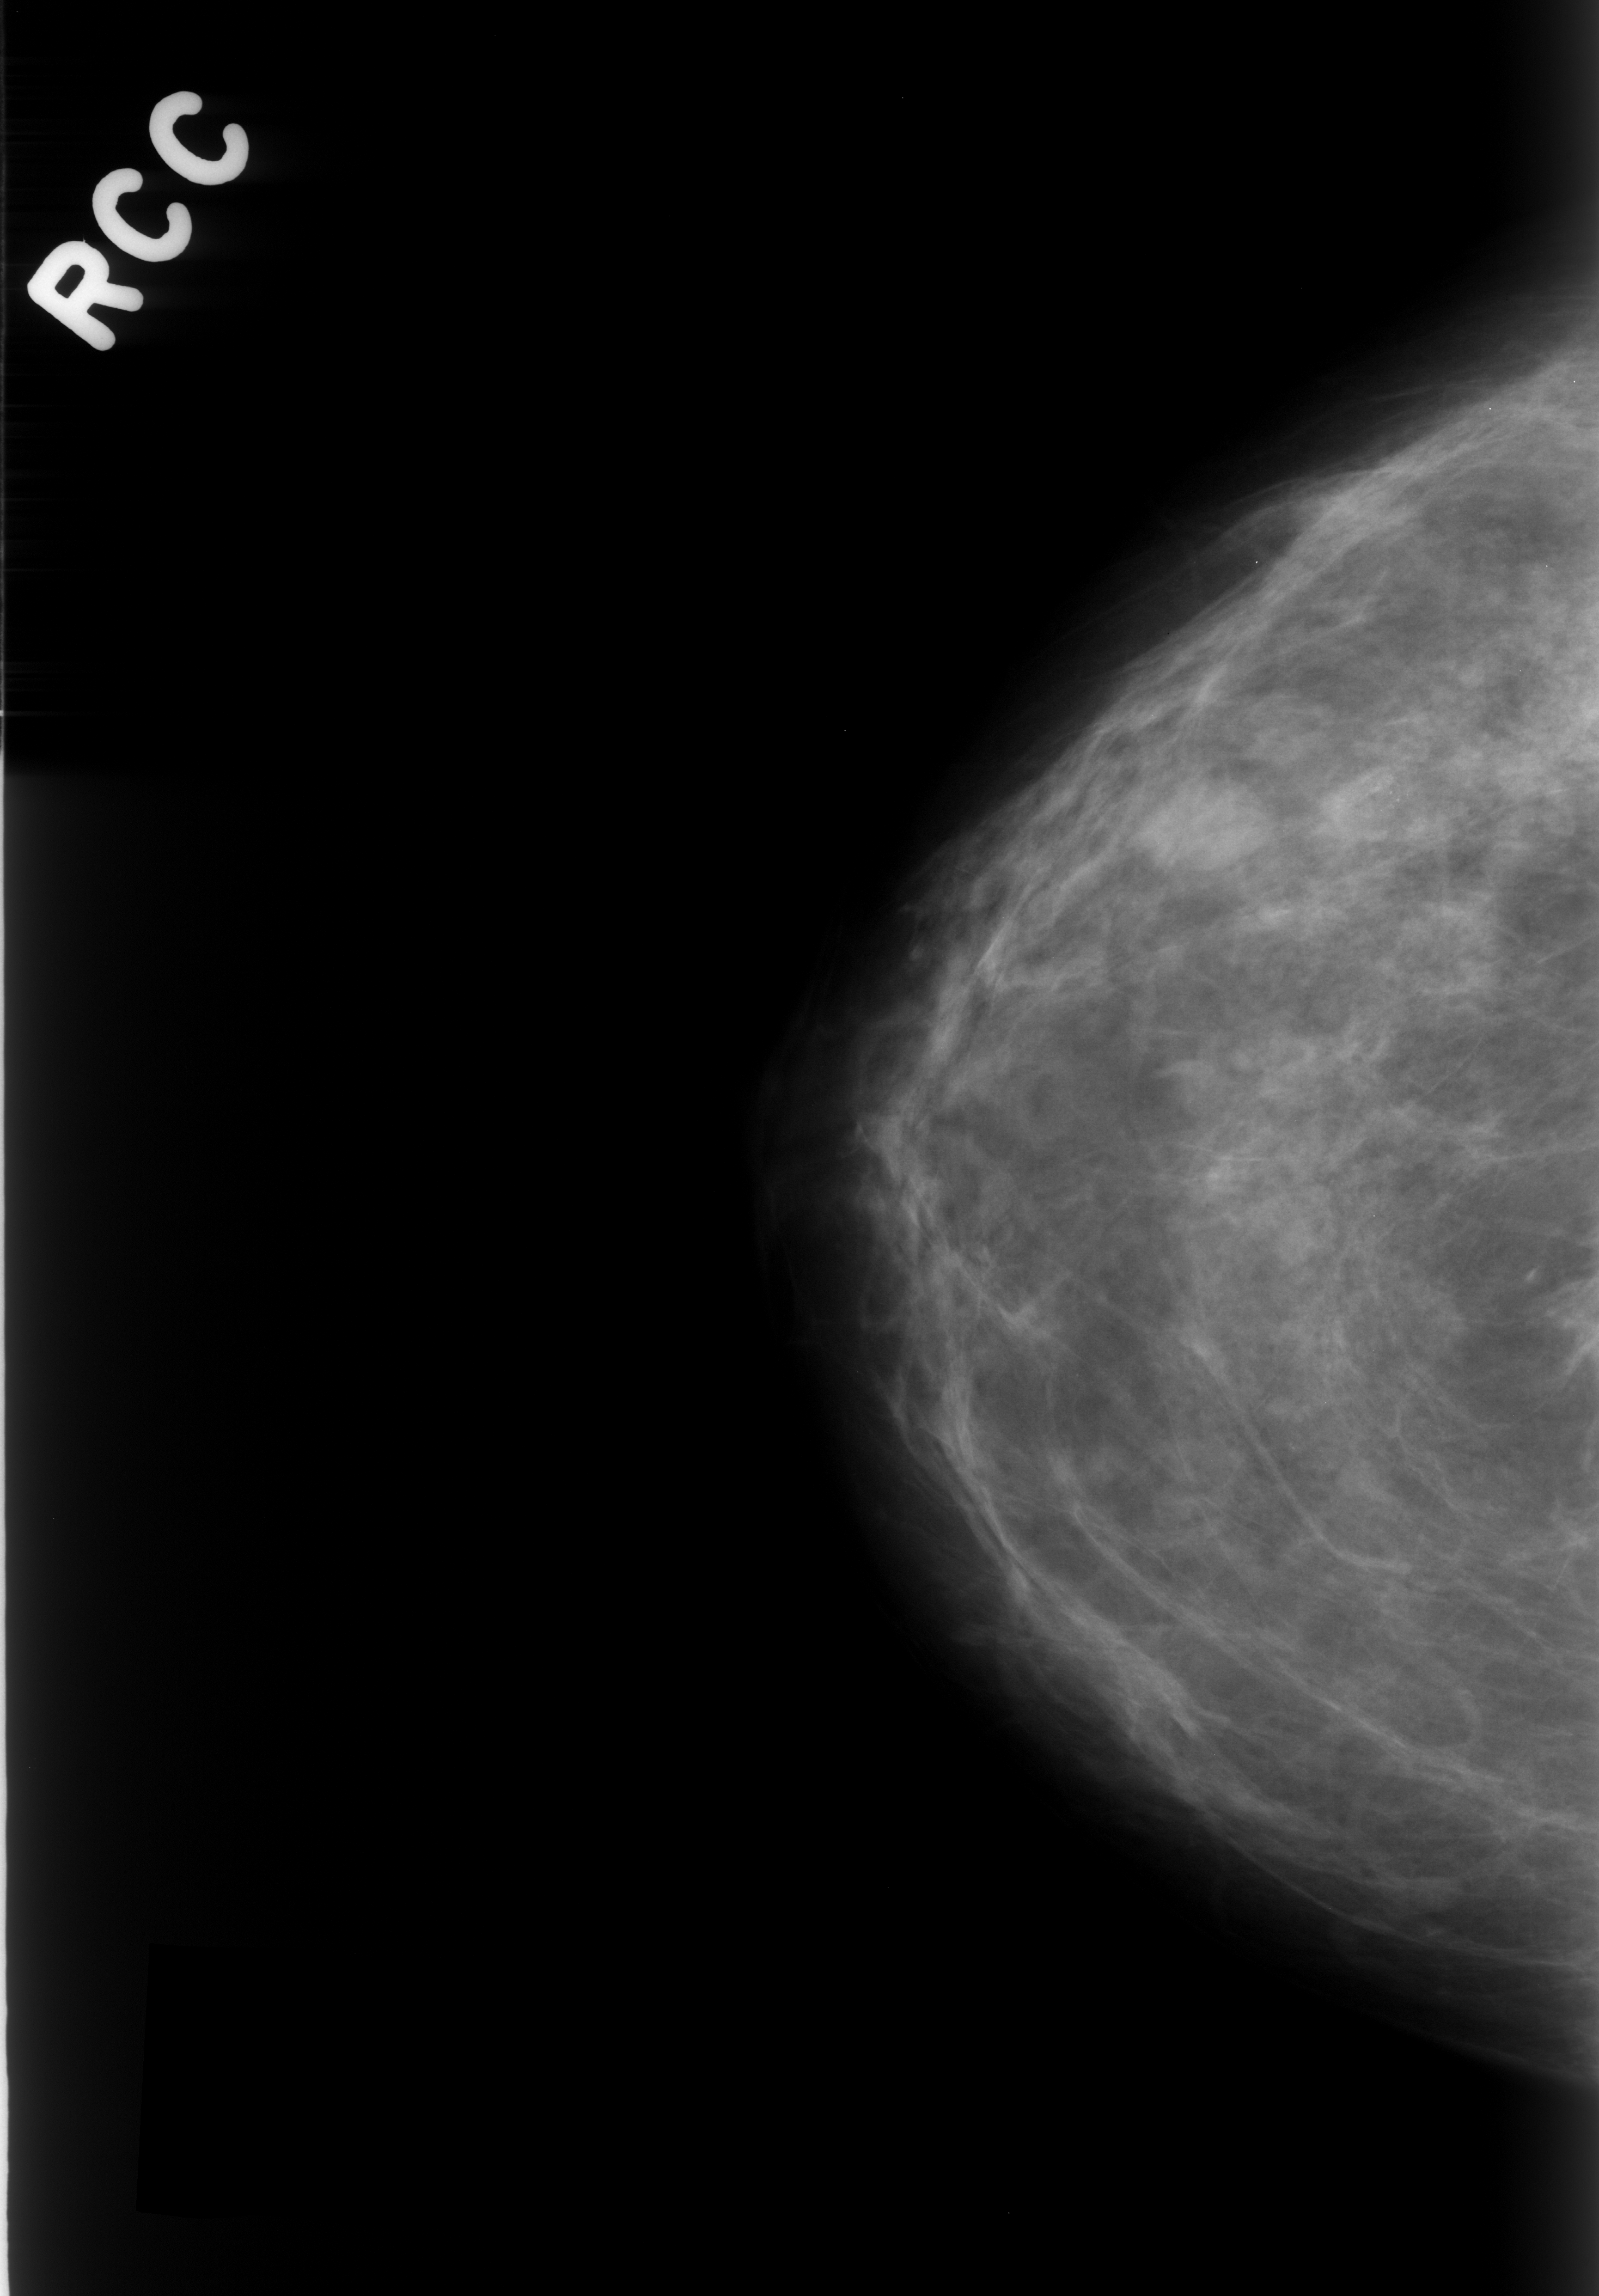
Digitized screen-film mammogram; right breast; craniocaudal (CC) view; BI-RADS breast density category 2 (scale 1–4); 1599 × 2296 image matrix.
Expert-marked regions of interest on this image (one box per marked abnormality):
- mass, shape oval, margins circumscribed; BI-RADS assessment category 3; pathology result (as recorded, not read from the image): benign: bounding box <1130,782,1267,899> (left, top, right, bottom; pixels)